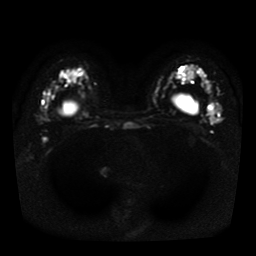
Breast MRI, one axial slice. Position 28 of 41 along the scan axis. Diffusion-weighted series; image 2 of 4 stored at this slice position (different b-values; order by instance number). 1.5 T. 5 mm slice thickness. 256 × 256 image matrix. Female patient.
Outlined on this slice (outlined manually by an expert reader):
- tumour on diffusion-weighted imaging: bounding box (x1, y1, x2, y2) in pixels: (206, 109, 216, 117)